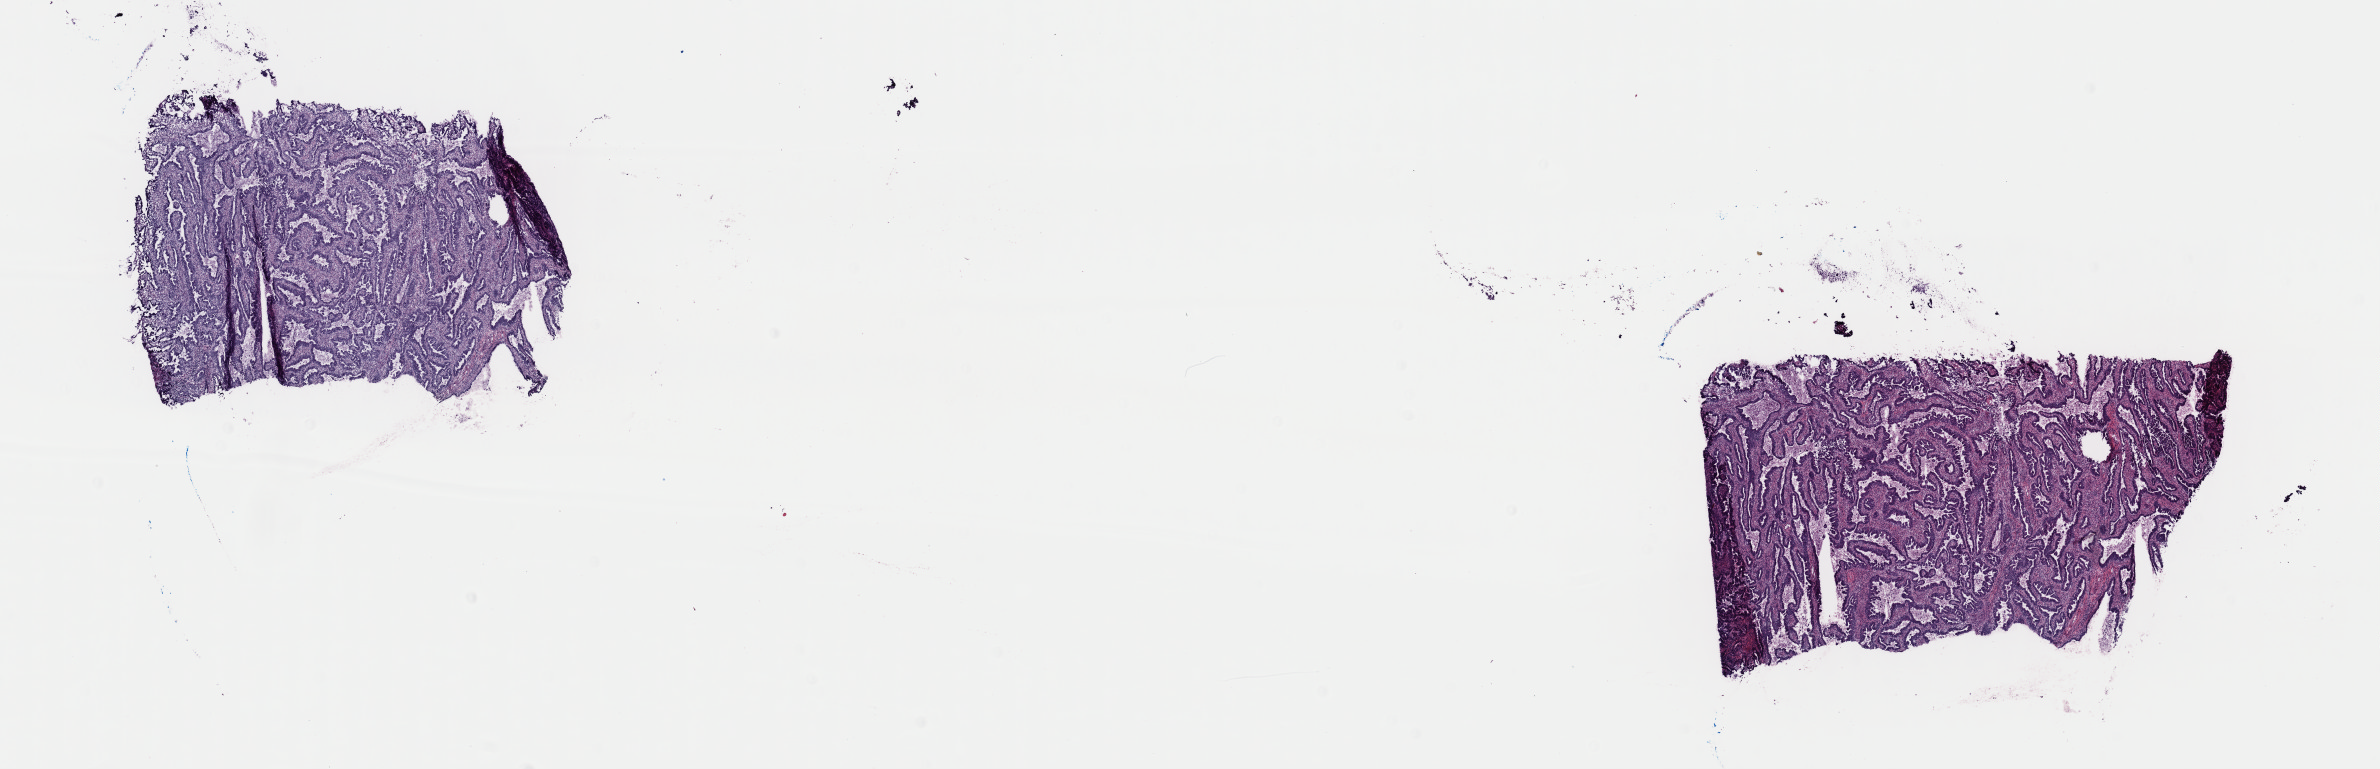
Whole-slide histology image, Hematoxylin and eosin (H&E) stained — a low-resolution overview of the entire scanned area, about 18.8 x 6.1 mm (acquisition: 40x scan). Frozen section. Cervix, primary tumour sample. Female, age 38 years at initial diagnosis. Histologic grade: G3 (poorly differentiated). Composition of this section per pathologist review: tumour cells 99%, tumour nuclei 75%, normal cells 0%, stromal cells 0%, necrosis 1%. Inflammatory infiltration, as recorded: lymphocyte infiltration 3%, monocyte infiltration 0%, neutrophil infiltration 0%.
FIGO stage: IIIB. Pathologic diagnosis: Adenocarcinoma, endocervical type (cervix uteri).